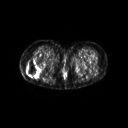
FDG PET of an extremity soft-tissue mass (from a PET/CT study), one axial slice. Slice 28 of 267 in the series (ordered by position). 3.27 mm slice thickness. 128 × 128 image matrix, field of view 600 × 600 mm. Patient: female, 57 years. From the clinical record (not read from this slice): histological type: epithelioid sarcoma with vascular differentiation; site of the primary tumour: right buttock.
Structures marked on this image (expert contour drawn on MRI and transferred to this co-registered scan by the dataset authors):
- gross tumour volume (mass): bounding box [x1, y1, x2, y2] px = [26, 60, 39, 76]